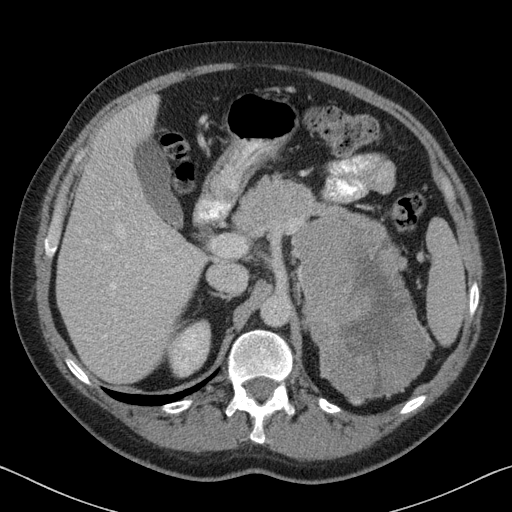
Contrast-enhanced abdominal CT, one axial slice. Reconstruction kernel B31f. 120 kVp. Intravenous contrast given. Soft-tissue window (W 400 / L 40 HU). 3 mm slice thickness. 512 × 512 image matrix, field of view 366 × 366 mm. Patient: male, 51 years. Case-level facts recorded for this patient, not image findings: diagnosis: adrenocortical carcinoma; tumour side: left adrenal; tumour size at pathology: 16.5 cm; Ki-67 index: 30 %; stage (as recorded): 2.
Outlined on this slice (semi-automatically segmented with operator editing):
- mass: bounding box (x1, y1, x2, y2) in pixels: (293, 219, 431, 405)